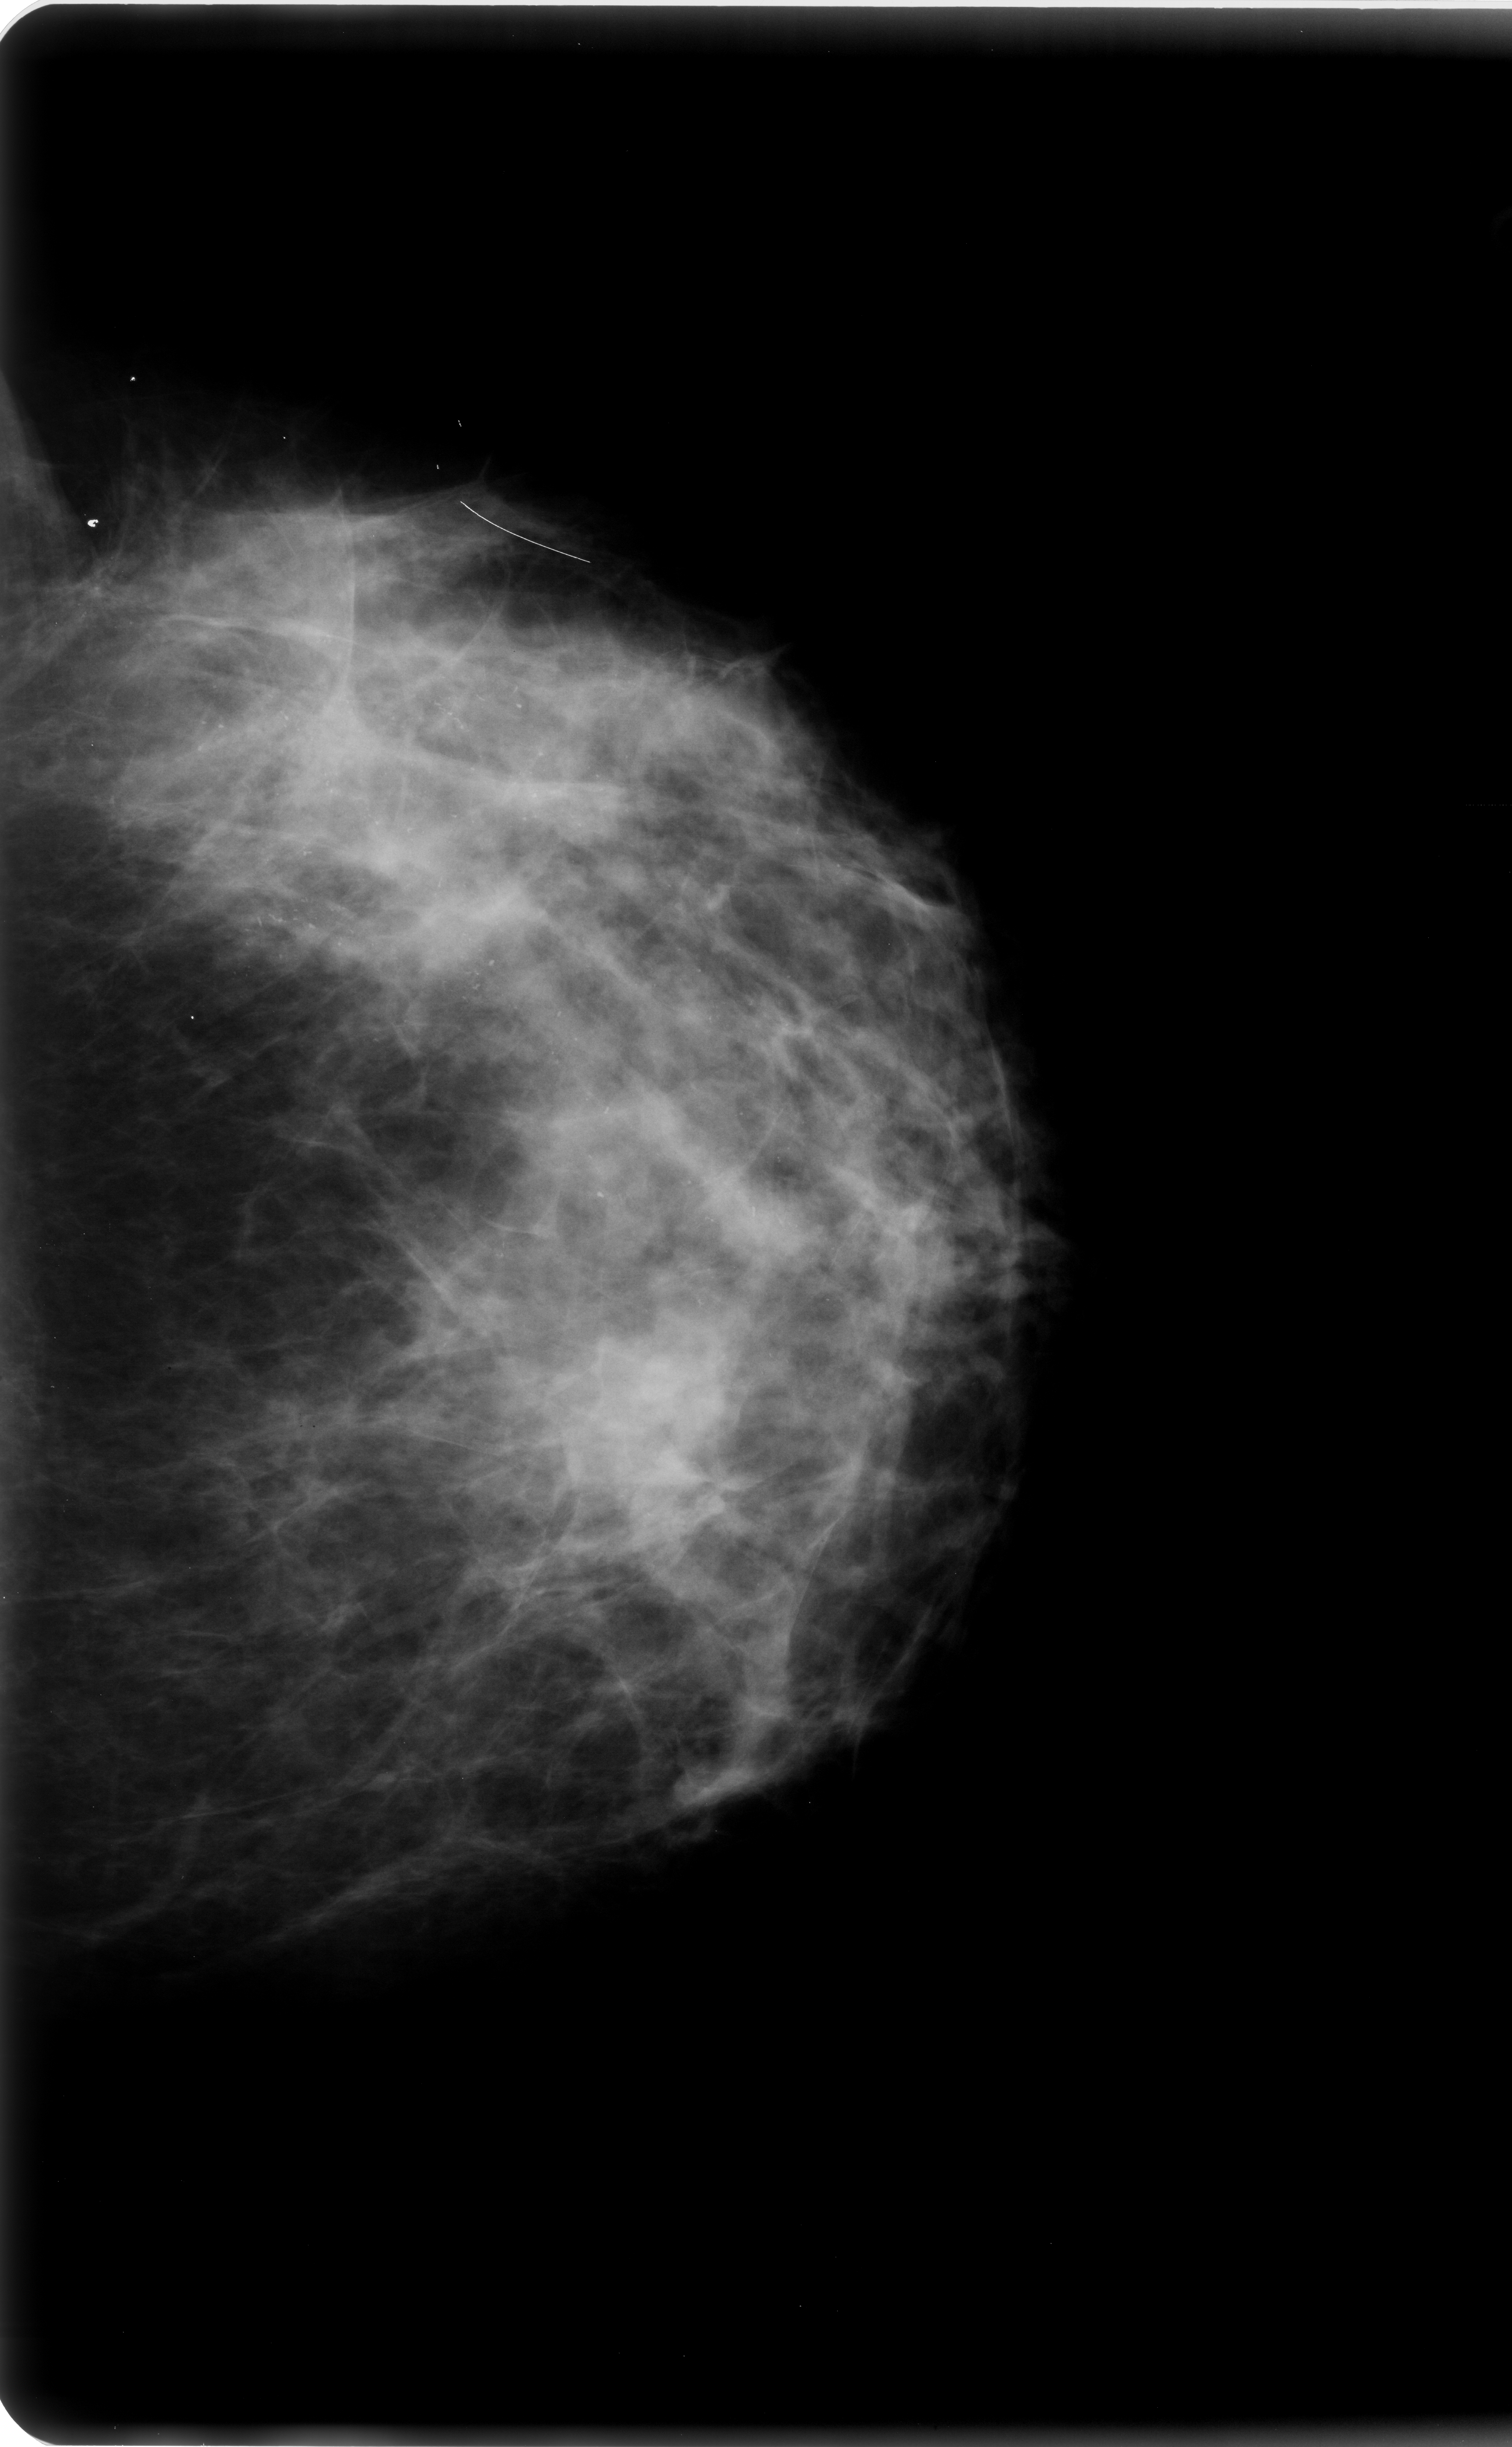
Scanned film-screen mammogram; left breast; craniocaudal (CC) view; breast composition: scattered fibroglandular densities (BI-RADS density category 2 of 4).
- Radiologist-marked abnormalities on this image: calcifications, morphology pleomorphic, distribution regional; BI-RADS assessment category 5; pathology result (as recorded, not read from the image): malignant.